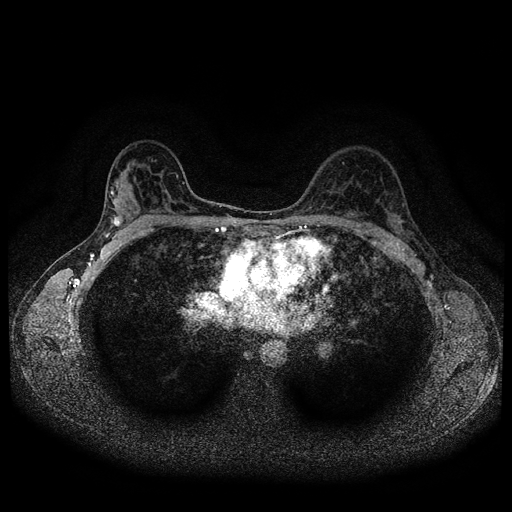
Breast MRI (dynamic contrast-enhanced, multi-phase), one axial slice; position 64 of 116 along the scan axis; dynamic contrast-enhanced series, time point 2 of 5 at this slice position (early post-contrast); 1.5 T; TE 2.7 ms, TR 5.4 ms; 512 × 512 image matrix, field of view 330 × 330 mm. Patient: female, 36 years.
Annotated regions visible in this slice (semi-automatically segmented with operator editing):
- breast lesion (labelled 'tumour' in the annotation; benign lesions carry a separate 'benign' label): box from (x=111, y=215) to (x=122, y=229) px